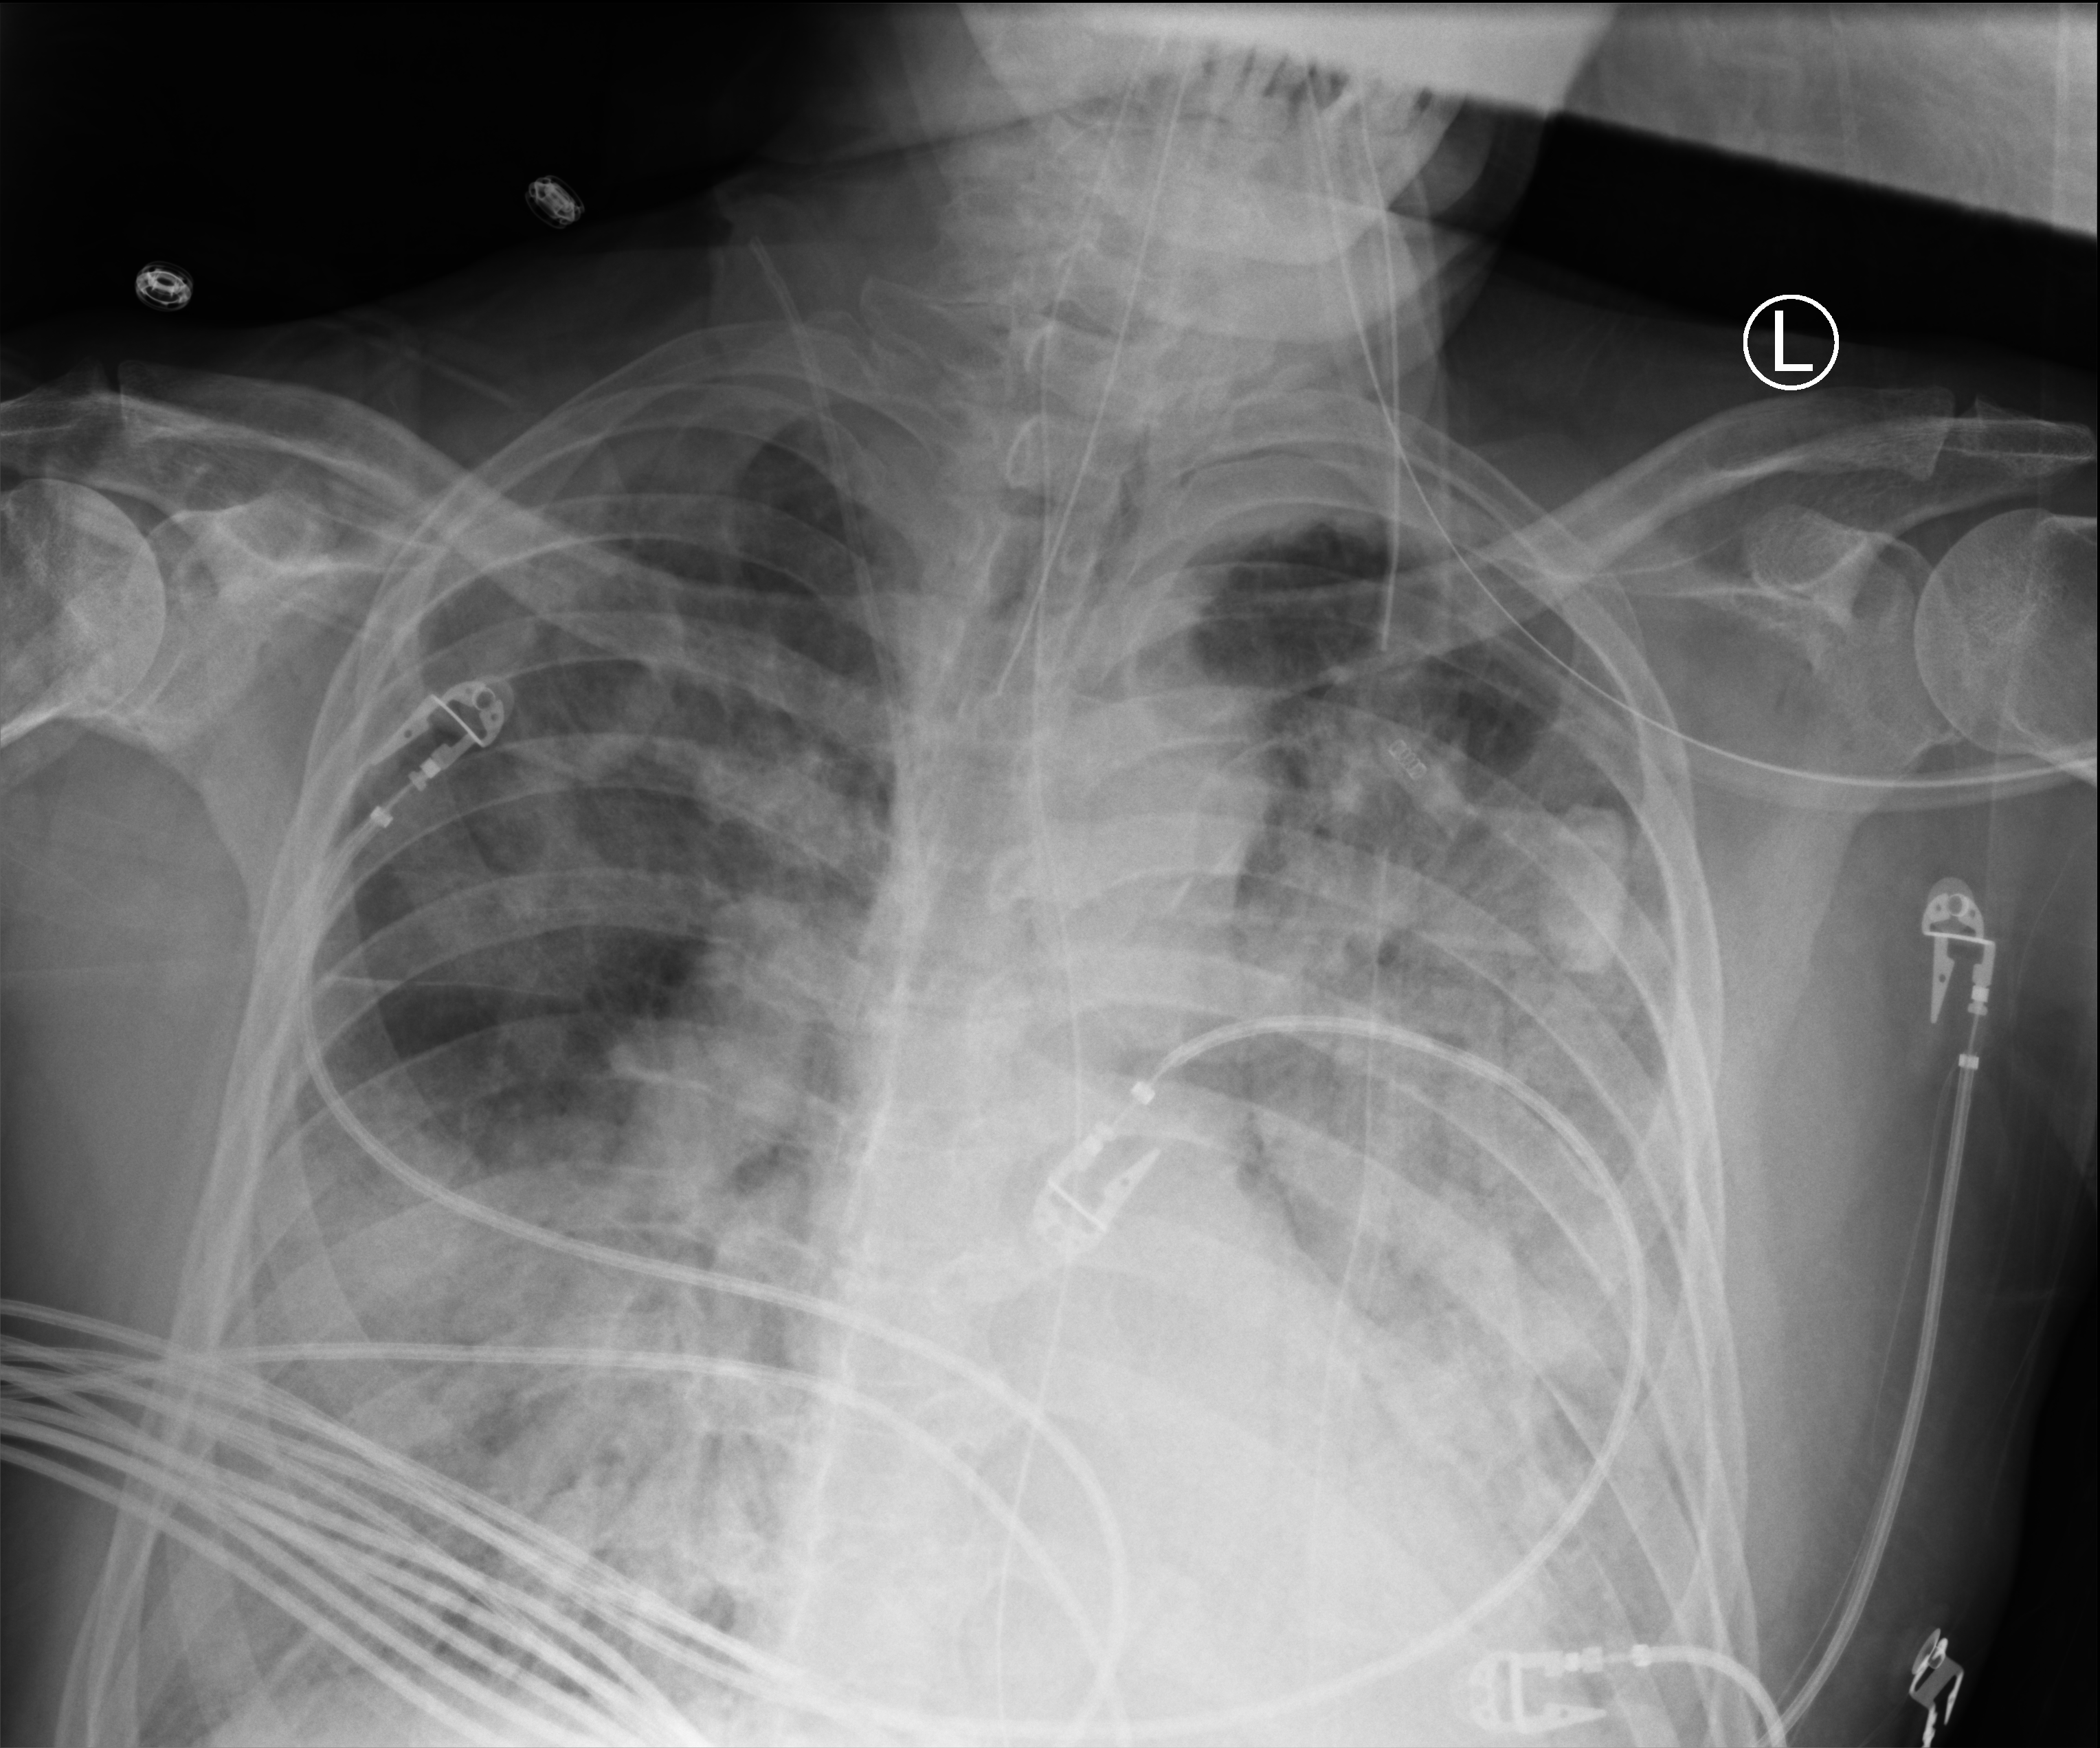
Portable chest radiograph; anteroposterior (AP) projection. Patient hospitalised with COVID-19; male, aged 60–74 years.
From the hospital-stay record, not from the radiograph (when in the stay this image was taken is not recorded): mechanically ventilated during this hospital stay: yes.